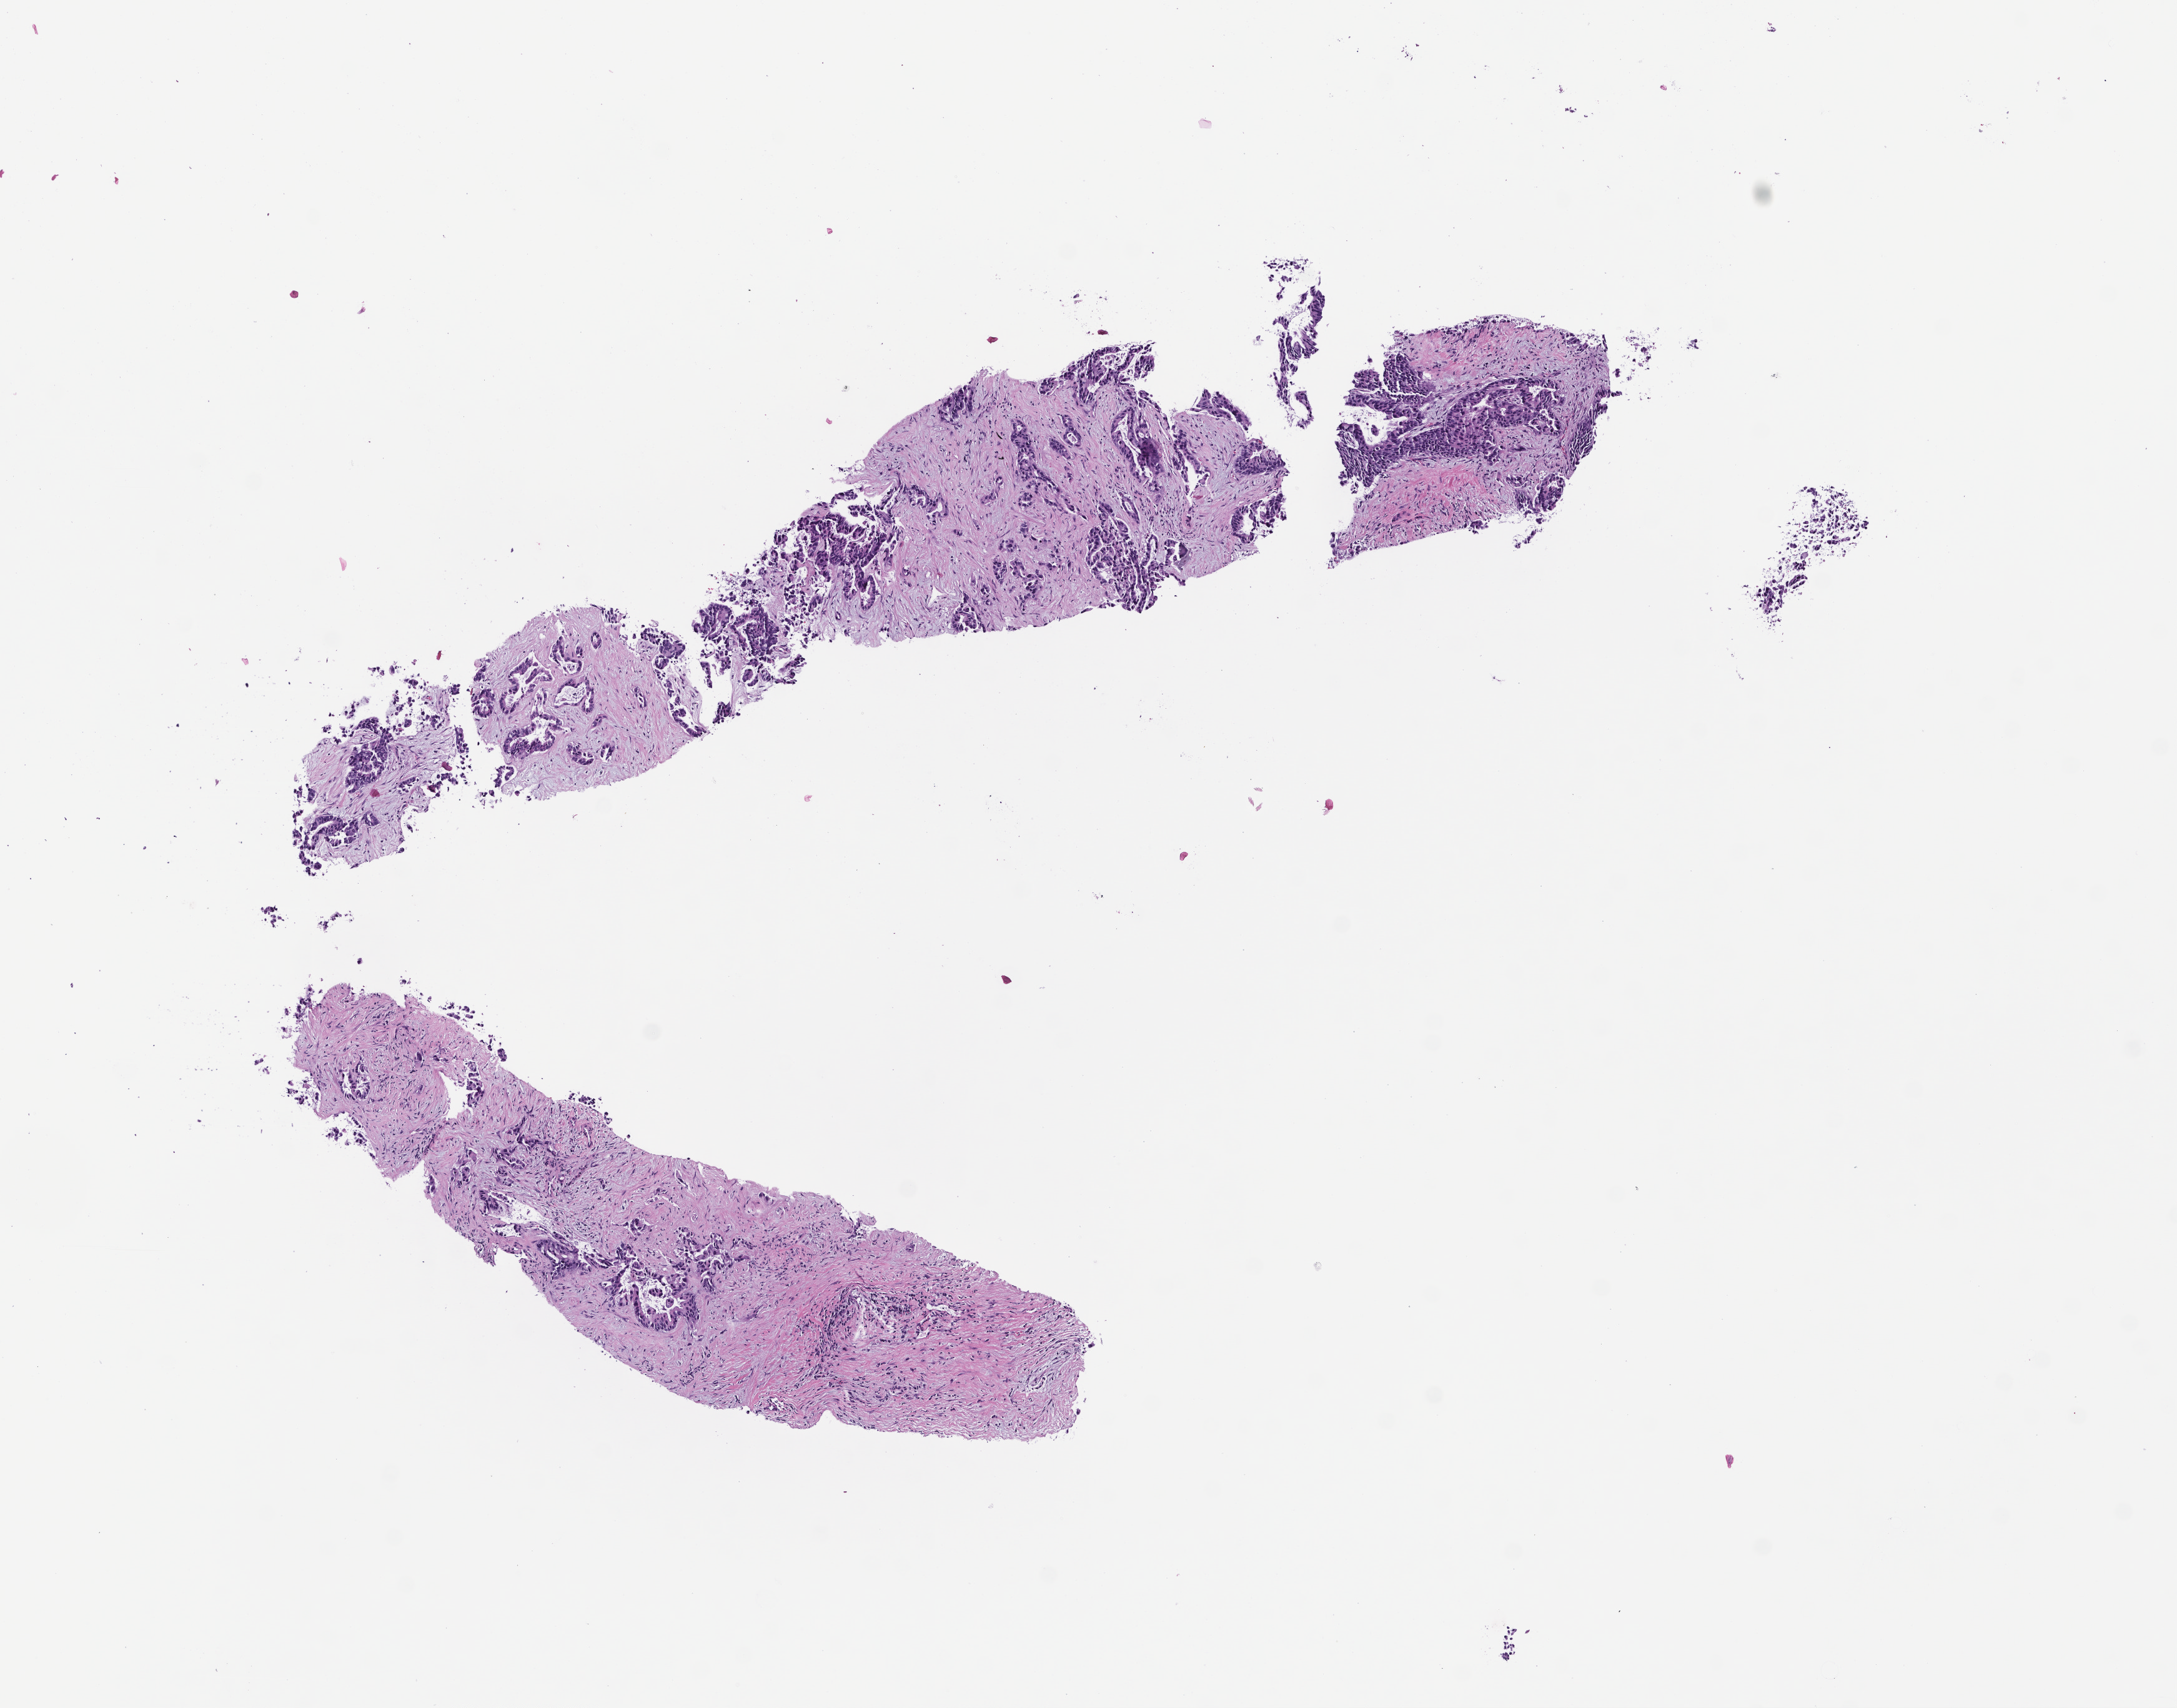
Whole-slide image, haematoxylin and eosin stain, whole scanned area (about 7.0 x 5.5 mm) shown as a low-resolution overview; FFPE section; collected at baseline (before treatment). Patient: female.
This section: metastatic tumor tissue. Primary diagnosis of the patient: Non-Small Cell Lung Carcinoma.